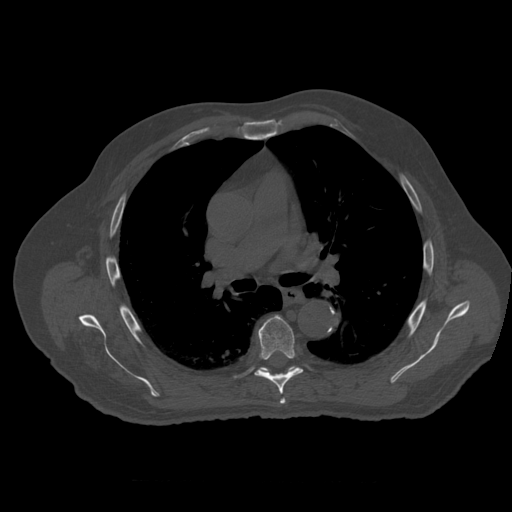
CT including the spine, one axial slice; position 379 of 399 along the scan axis; reconstruction kernel STANDARD; 120 kVp; bone window (W 1800 / L 400 HU); 1.25 mm slice thickness; 512 × 512 image matrix, field of view 407 × 407 mm. Patient age 73 years. Case-level facts recorded for this patient, not image findings: primary cancer: prostate; vertebrae with lytic lesions (as recorded): L2.
Outlined on this slice (semi-automatic segmentation, software-assisted and operator-edited):
- T5 vertebra: bounding box <280,398,286,404> (left, top, right, bottom; pixels)
- T6 vertebra: <255,316,303,395>
- T7 vertebra: <259,367,296,374>